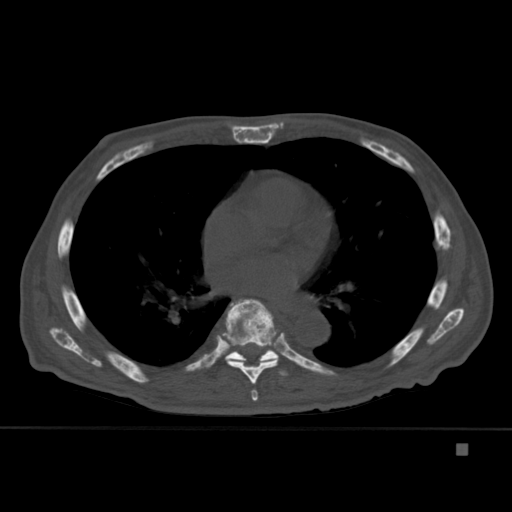
CT including the spine, one axial slice; position 274 of 451 along the scan axis; bone window (W 1800 / L 400 HU); 1.5 mm slice thickness; 512 × 512 image matrix, field of view 378 × 378 mm. Male patient, age 75 years. Case-level facts recorded for this patient, not image findings: primary cancer: prostate.
Outlined on this slice (semi-automatic segmentation, software-assisted and operator-edited):
- T6 vertebra: bounding box <251,389,258,401> (left, top, right, bottom; pixels)
- T7 vertebra: <222,299,281,385>
- T8 vertebra: <225,299,288,376>